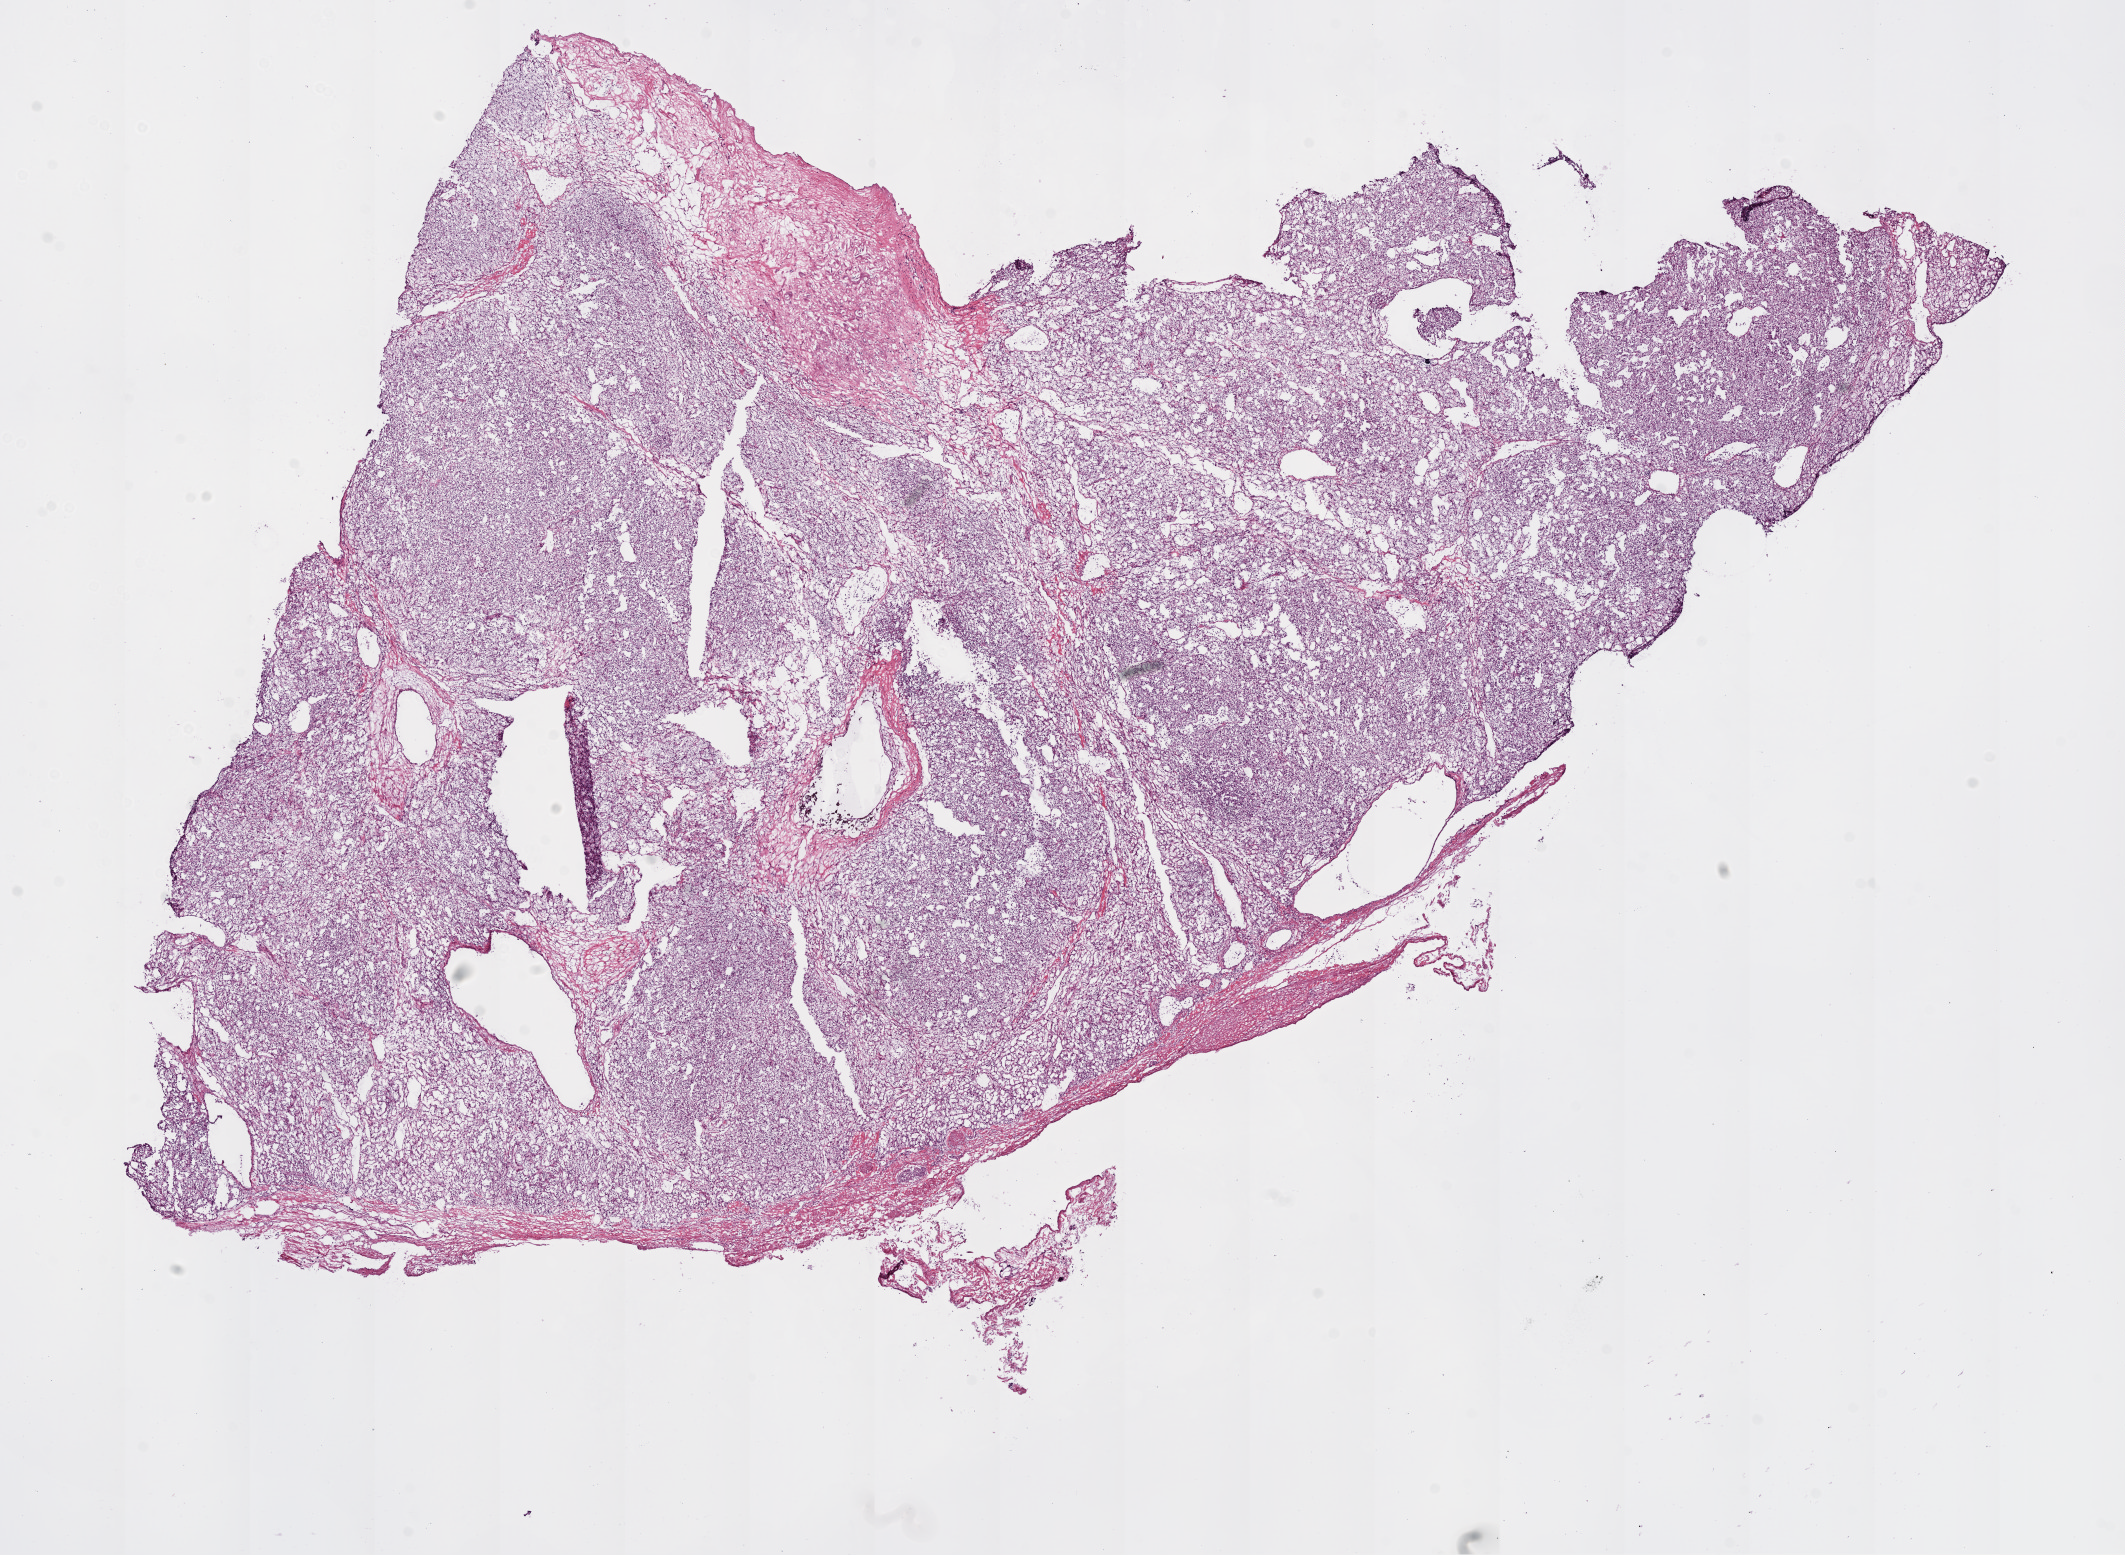
Hematoxylin and eosin (H&E) stained whole-slide image, low-resolution overview of the scanned area, about 17.1 x 12.5 mm (acquisition: 20x scan). Frozen section from the bottom of the tissue portion. Primary tumour sample from the kidney. Male, age 59 years at initial diagnosis. Histologic grade: G2 (moderately differentiated). Composition of this section per pathologist review: tumour cells 85%, tumour nuclei 85%, normal cells 0%, stromal cells 15%, necrosis 0%.
AJCC pathologic stage: I. TNM: T1a NX M0. Histologic diagnosis: Clear cell adenocarcinoma, NOS. Laterality: right.